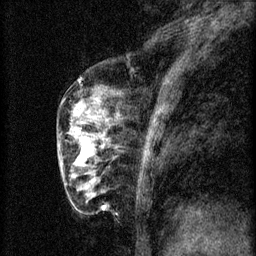
Breast MRI (dynamic contrast-enhanced), one sagittal slice; slice 23 of 60 in the series (ordered by position); 3 images stored at this slice position (order not interpretable as contrast timing); 1.5 T; TE 4.2 ms, TR 8.2 ms; 256 × 256 image matrix. Female patient, age 56 years.
Outlined on this slice (semi-automatic segmentation, software-assisted and operator-edited):
- analysis volume of interest (the breast-tissue region the enhancement analysis was run in; not a lesion): bounding box (x1, y1, x2, y2) in pixels: (60, 124, 114, 179)
- tumour enhancement mask (voxels above the 70 % enhancement threshold inside the analysis volume of interest): (78, 138, 93, 167)